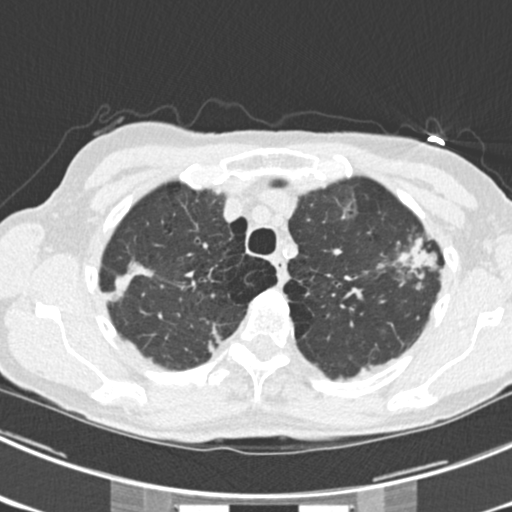
Low-dose screening chest CT, one axial slice; position 178 of 225 along the scan axis; lung window (W 1500 / L -600 HU); 512 × 512 image matrix, field of view 302 × 302 mm.
Outlined on this slice (expert manual segmentation):
- lesion 1 (tumor, upper lobe of left lung): bounding box <395,237,437,270> (left, top, right, bottom; pixels)
- lesion 5 (tumor, upper lobe of right lung): <109,263,154,302>